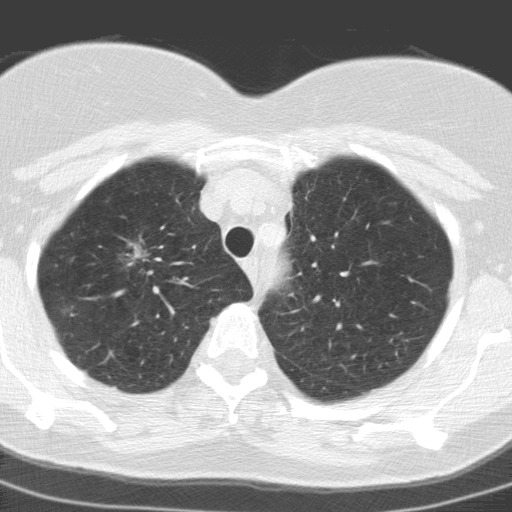
Axial slice from a low-dose chest CT screening exam; baseline annual screen; lung window (W 1500 / L -600 HU); standard (soft-tissue) reconstruction kernel (C). Female, age 60 years at enrolment. Former smoker at enrolment.
Lesion marked by an expert reader, box from (x=104, y=230) to (x=158, y=276) px. Screening reader's record for this exam: no non-calcified nodule ≥4 mm recorded. Official screen result: negative screen, minor abnormalities not suspicious for lung cancer. Lung cancer was diagnosed 447 days after this screen: adenocarcinoma, NOS, right upper lobe, moderately differentiated (G2), stage IA (AJCC 6th edition), 23 mm at pathology.